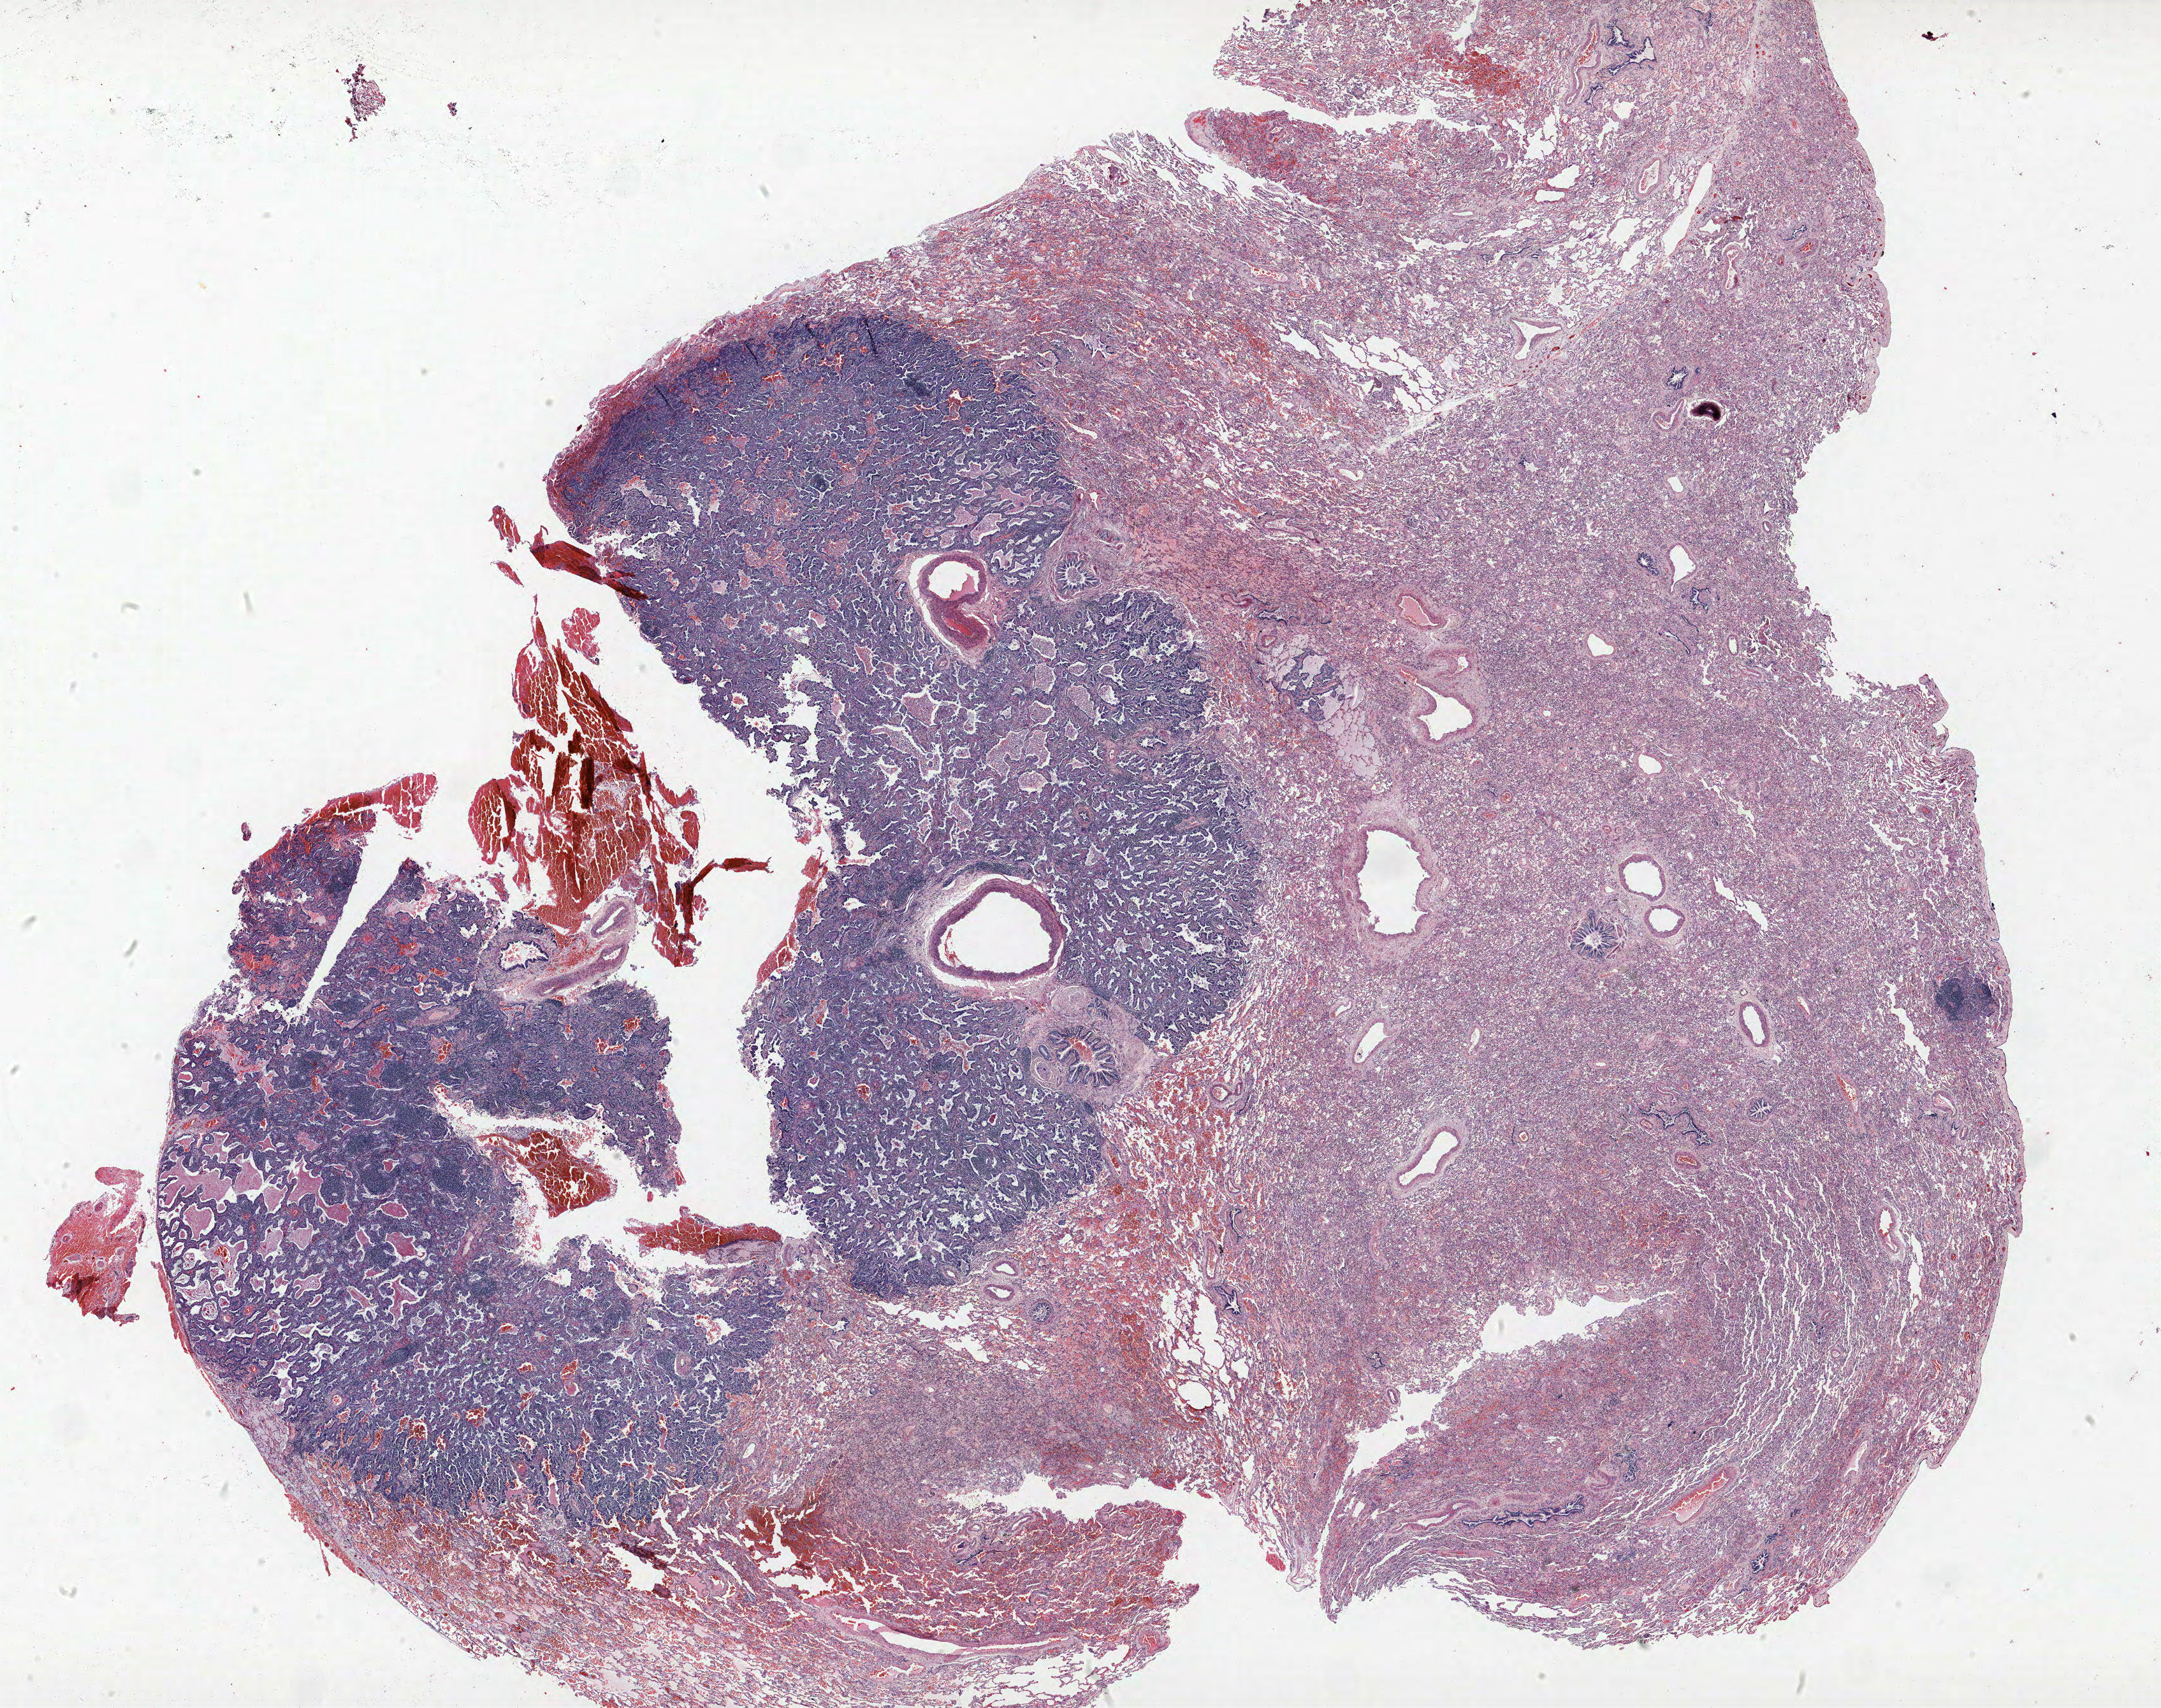
Whole-slide histology image, Hematoxylin and eosin (H&E) stained, low-resolution overview of the scanned area, about 27.1 x 21.4 mm. Formalin-fixed paraffin-embedded (FFPE) section. Lung tissue. Female patient, aged 60 at enrolment. Former smoker at enrolment.
- primary tumour location (clinical record): right lower lobe
- participant's lung-cancer diagnosis: Bronchiolo-alveolar carcinoma, non-mucinous
- ICD-O-3 topography: lower lobe of lung (C34.3)
- stage (AJCC 6th edition): IA
- tumour size (pathology): 15 mm